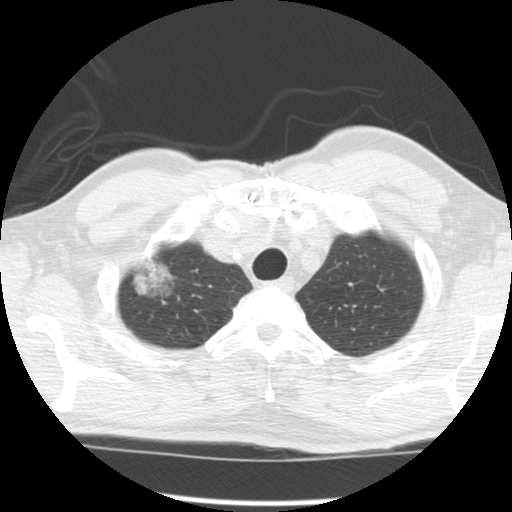
Chest CT (low-dose screening protocol), one axial image, second annual screen, lung window (W 1500 / L -600 HU), 2.5 mm slice thickness, standard (soft-tissue) reconstruction kernel (STANDARD), slice 15 of 120 in the series, 512 × 512 image matrix. Male, age 64 years at enrolment. Former smoker at enrolment.
Expert reader's lesion annotation, bounding box [x1, y1, x2, y2] px = [122, 240, 185, 308]. The screening reader recorded 2 non-calcified nodules or masses ≥4 mm on this exam (right upper lobe, left upper lobe); which of them this box marks is not recorded. Official screen result: positive, other. Later outcome: lung cancer diagnosed 429 days after this screen (after the third annual screen) — adenocarcinoma, NOS, right upper lobe, well differentiated (G1), stage IB (AJCC 6th edition), 45 mm at pathology.